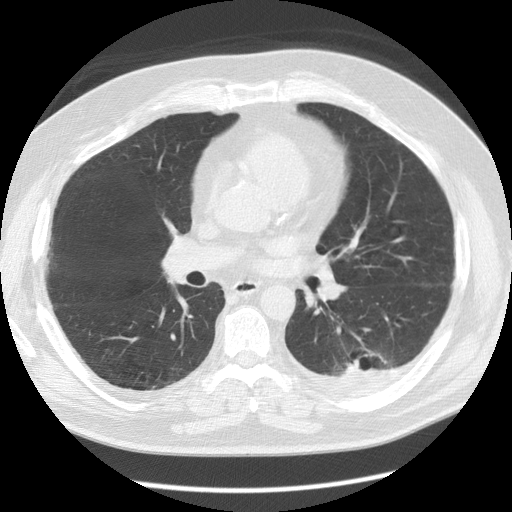
Low-dose screening chest CT, one axial slice; position 69 of 126 along the scan axis; lung window (W 1500 / L -600 HU); 2.5 mm slice thickness; 512 × 512 image matrix.
Outlined on this slice (expert manual segmentation):
- lesion 1 (tumor, lower lobe of left lung): bounding box (x1, y1, x2, y2) in pixels: (343, 359, 376, 375)